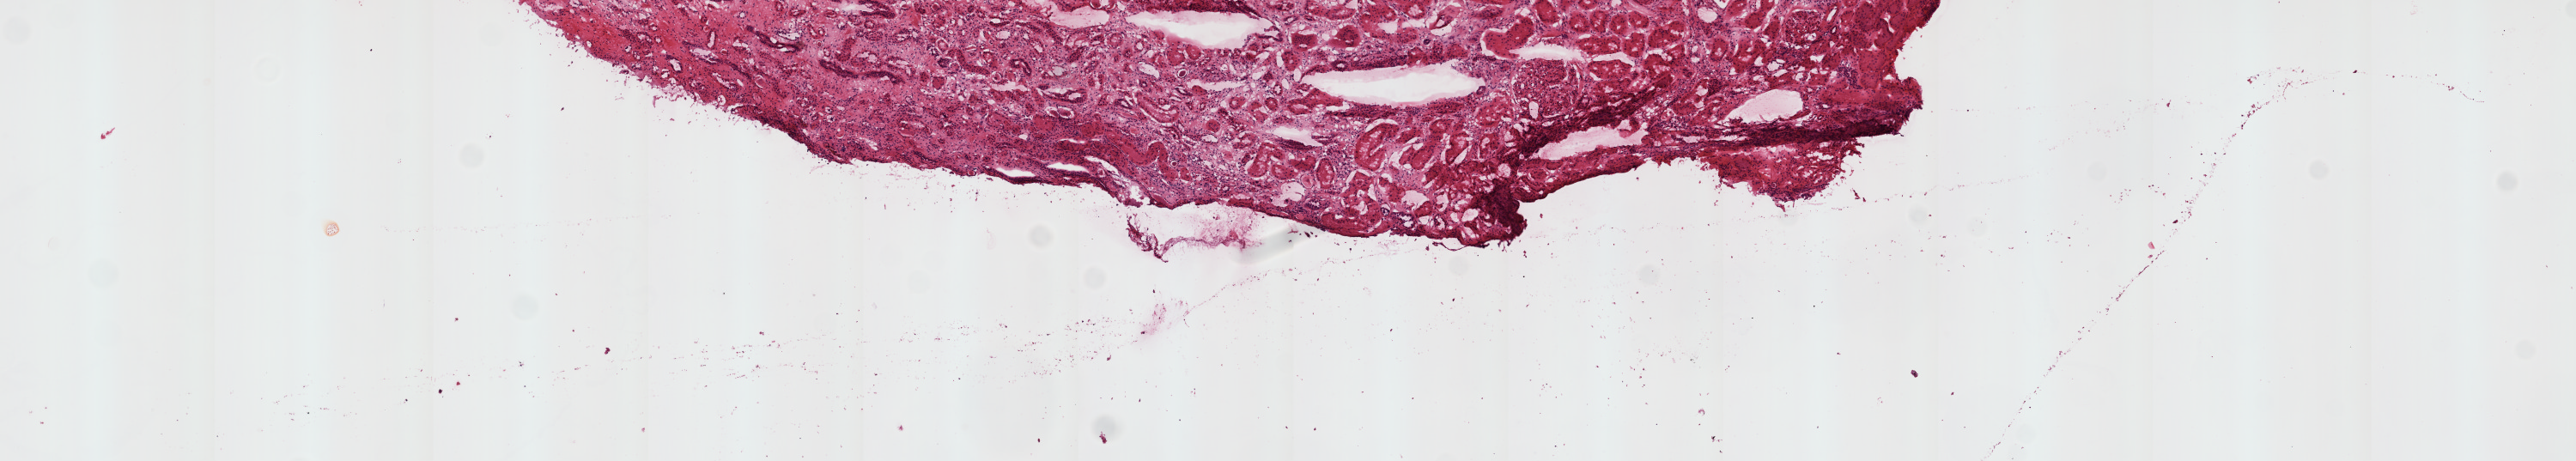
Digitized H&E tissue section (whole slide), low-resolution overview of the scanned area, about 12.0 x 2.2 mm, frozen section from the top of the tissue portion, kidney, solid tissue normal (non-tumour tissue) sample. Male, age 70 years at initial diagnosis.
This section: solid tissue normal (non-tumour) sample from the same patient. Patient diagnosis: Clear cell adenocarcinoma, NOS.